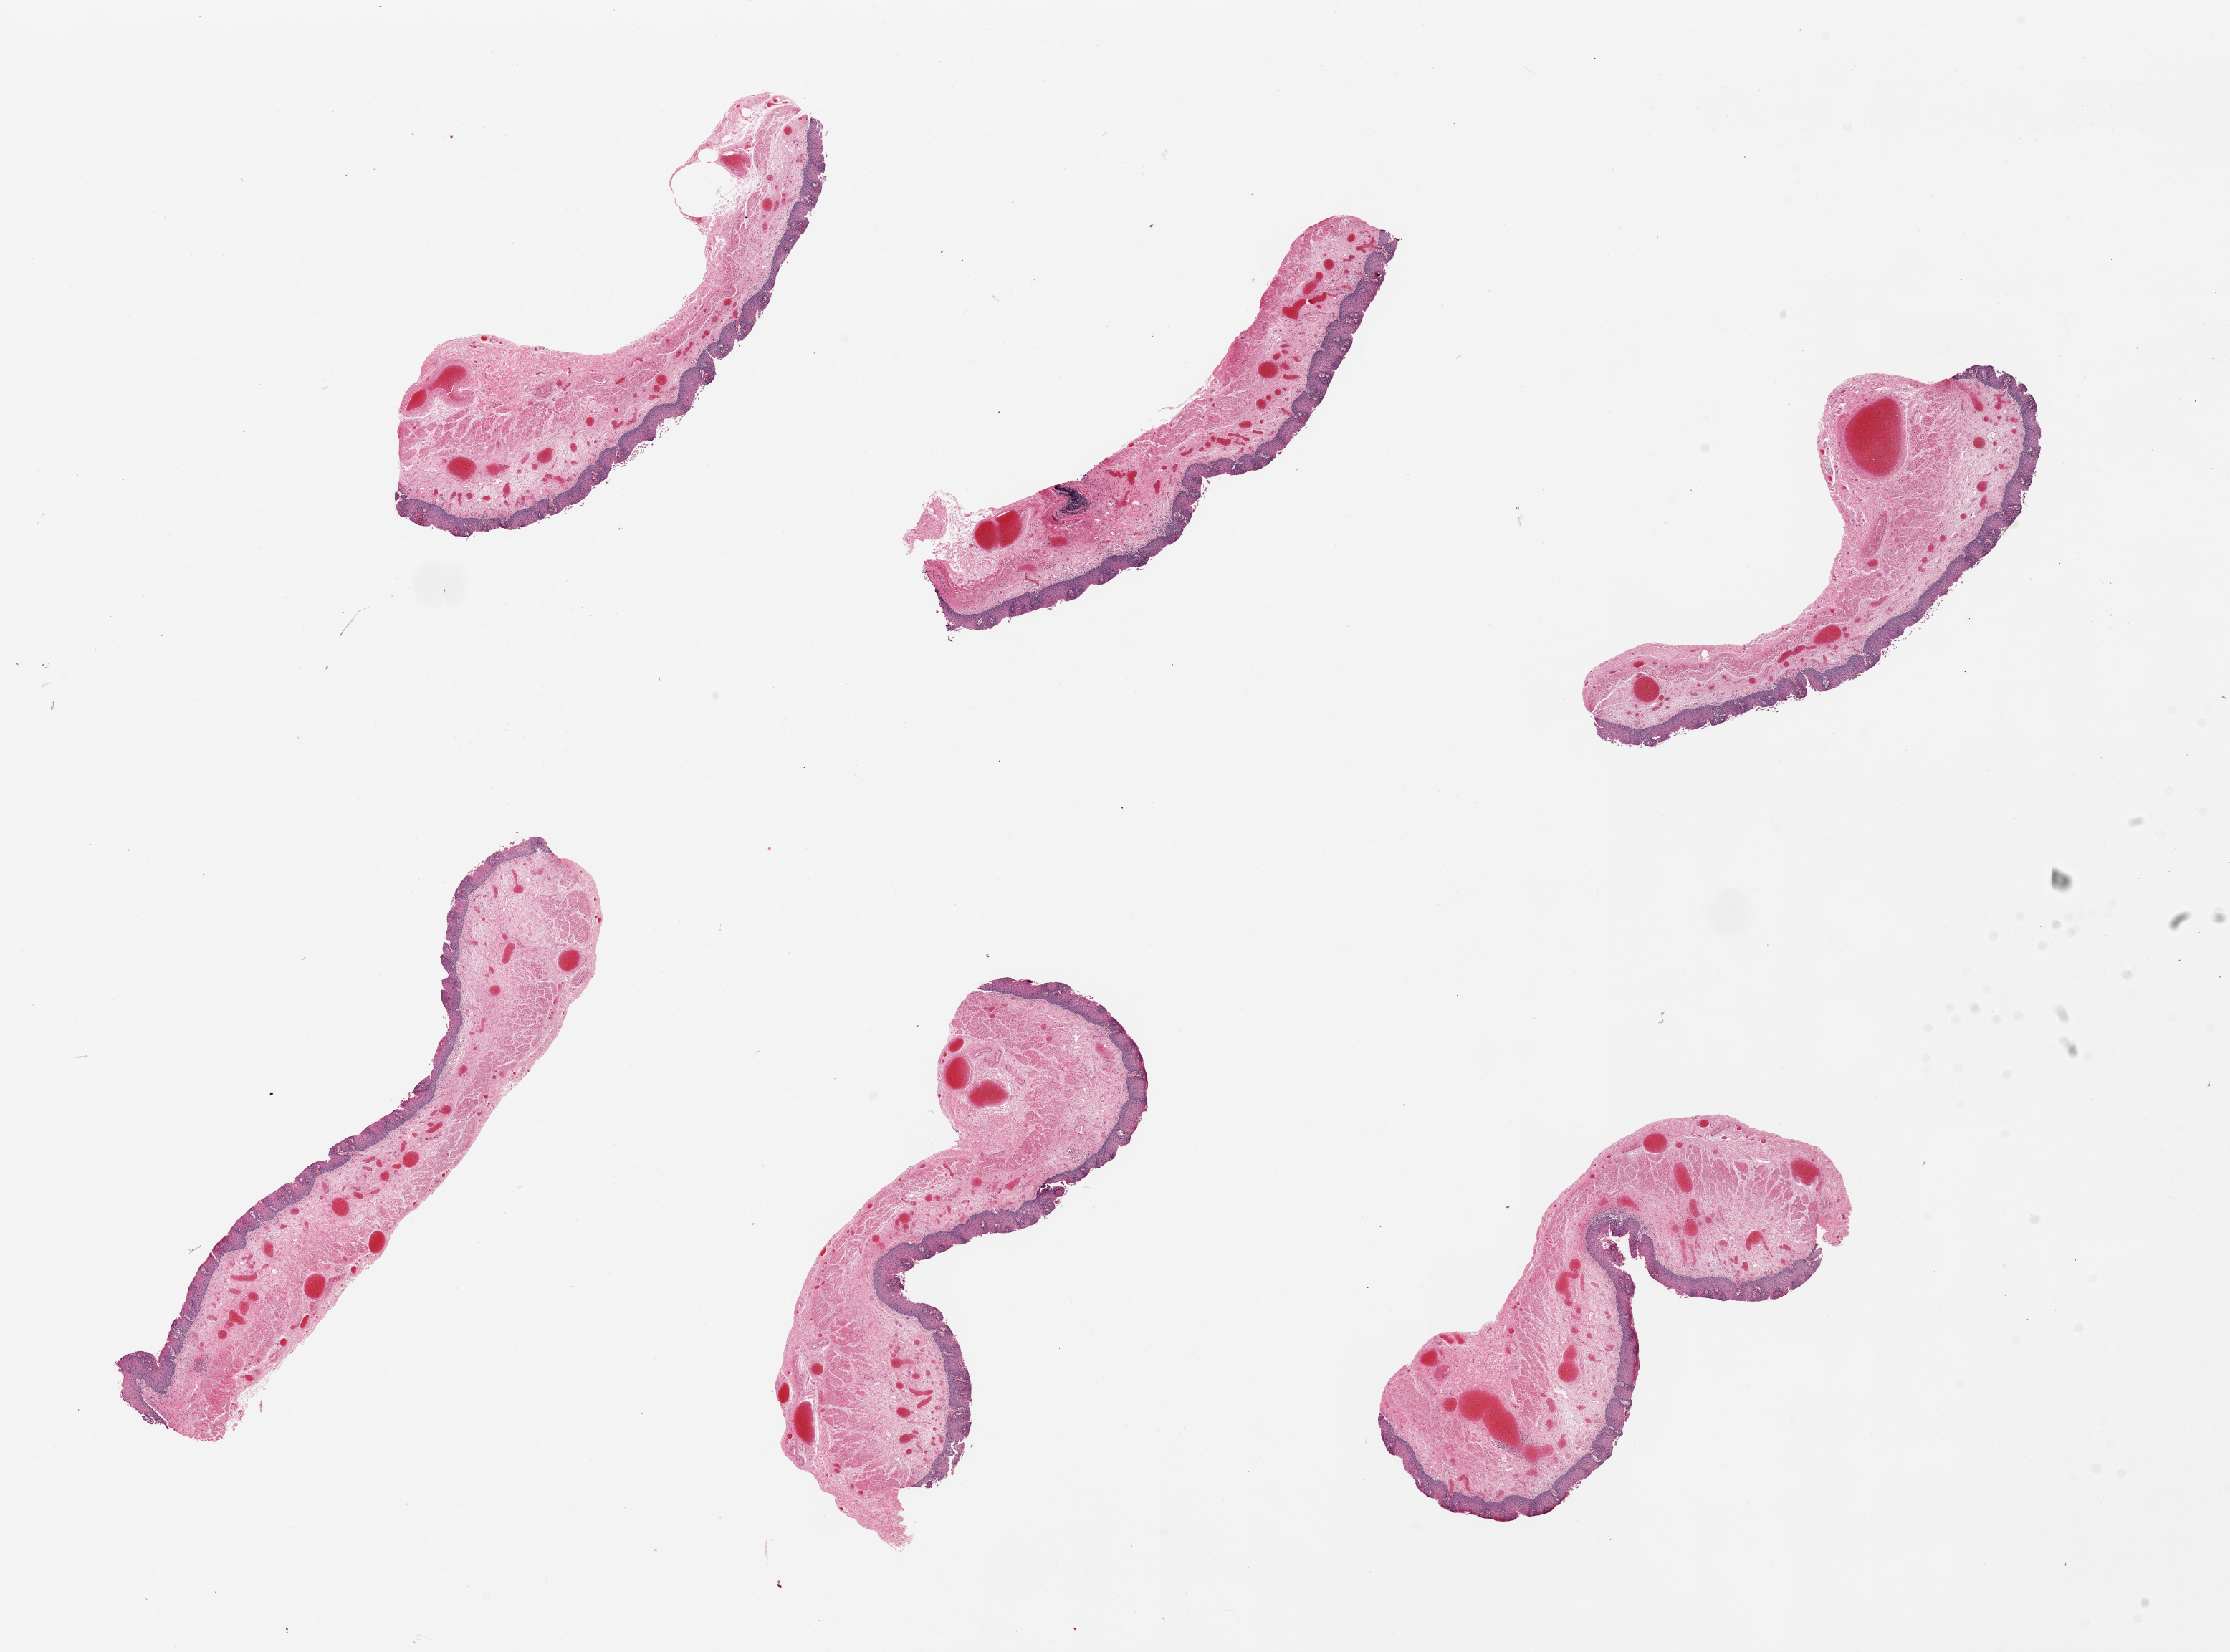
Digitized H&E-stained section, whole scanned area (about 24.6 x 18.2 mm, acquisition: 20x scan) shown as a low-resolution overview, PAXgene-fixed paraffin-embedded (PFPE) section, sampled site (target tissue): esophageal mucous membrane, tissue donor sample.
Pathologist's review note for this sample: 6 pieces; numerous dilated vessels within submucosa.